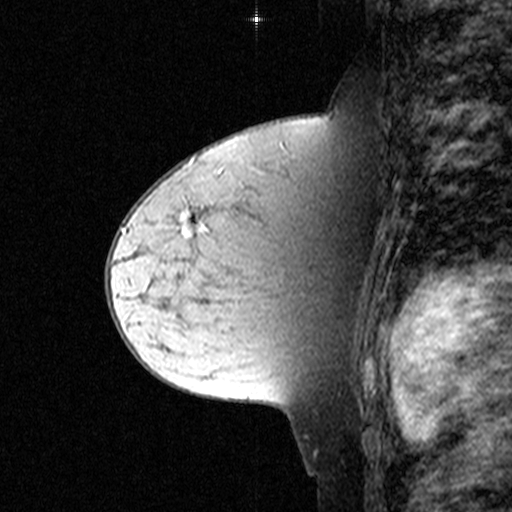
Breast MRI (dynamic contrast-enhanced), one sagittal slice. Slice 25 of 44 in the series (ordered by position). Dynamic contrast-enhanced study with each time point stored as its own series, time point 2 of 3 at this slice position (early post-contrast, ordered by acquisition time). 1.5 T. TE 4.5 ms, TR 11 ms. 512 × 512 image matrix, field of view 200 × 200 mm. Patient: female, 44 years. From the clinical record (not read from this slice): setting: breast cancer imaged before/during neoadjuvant chemotherapy; receptor status: triple-negative.
Structures marked on this image (semi-automatically segmented with operator editing):
- analysis volume of interest (the breast-tissue region the enhancement analysis was run in; not a lesion): bounding box (x1, y1, x2, y2) in pixels: (174, 204, 303, 305)
- tumour enhancement mask (voxels above the 90 % enhancement threshold inside the analysis volume of interest): (183, 214, 207, 235)